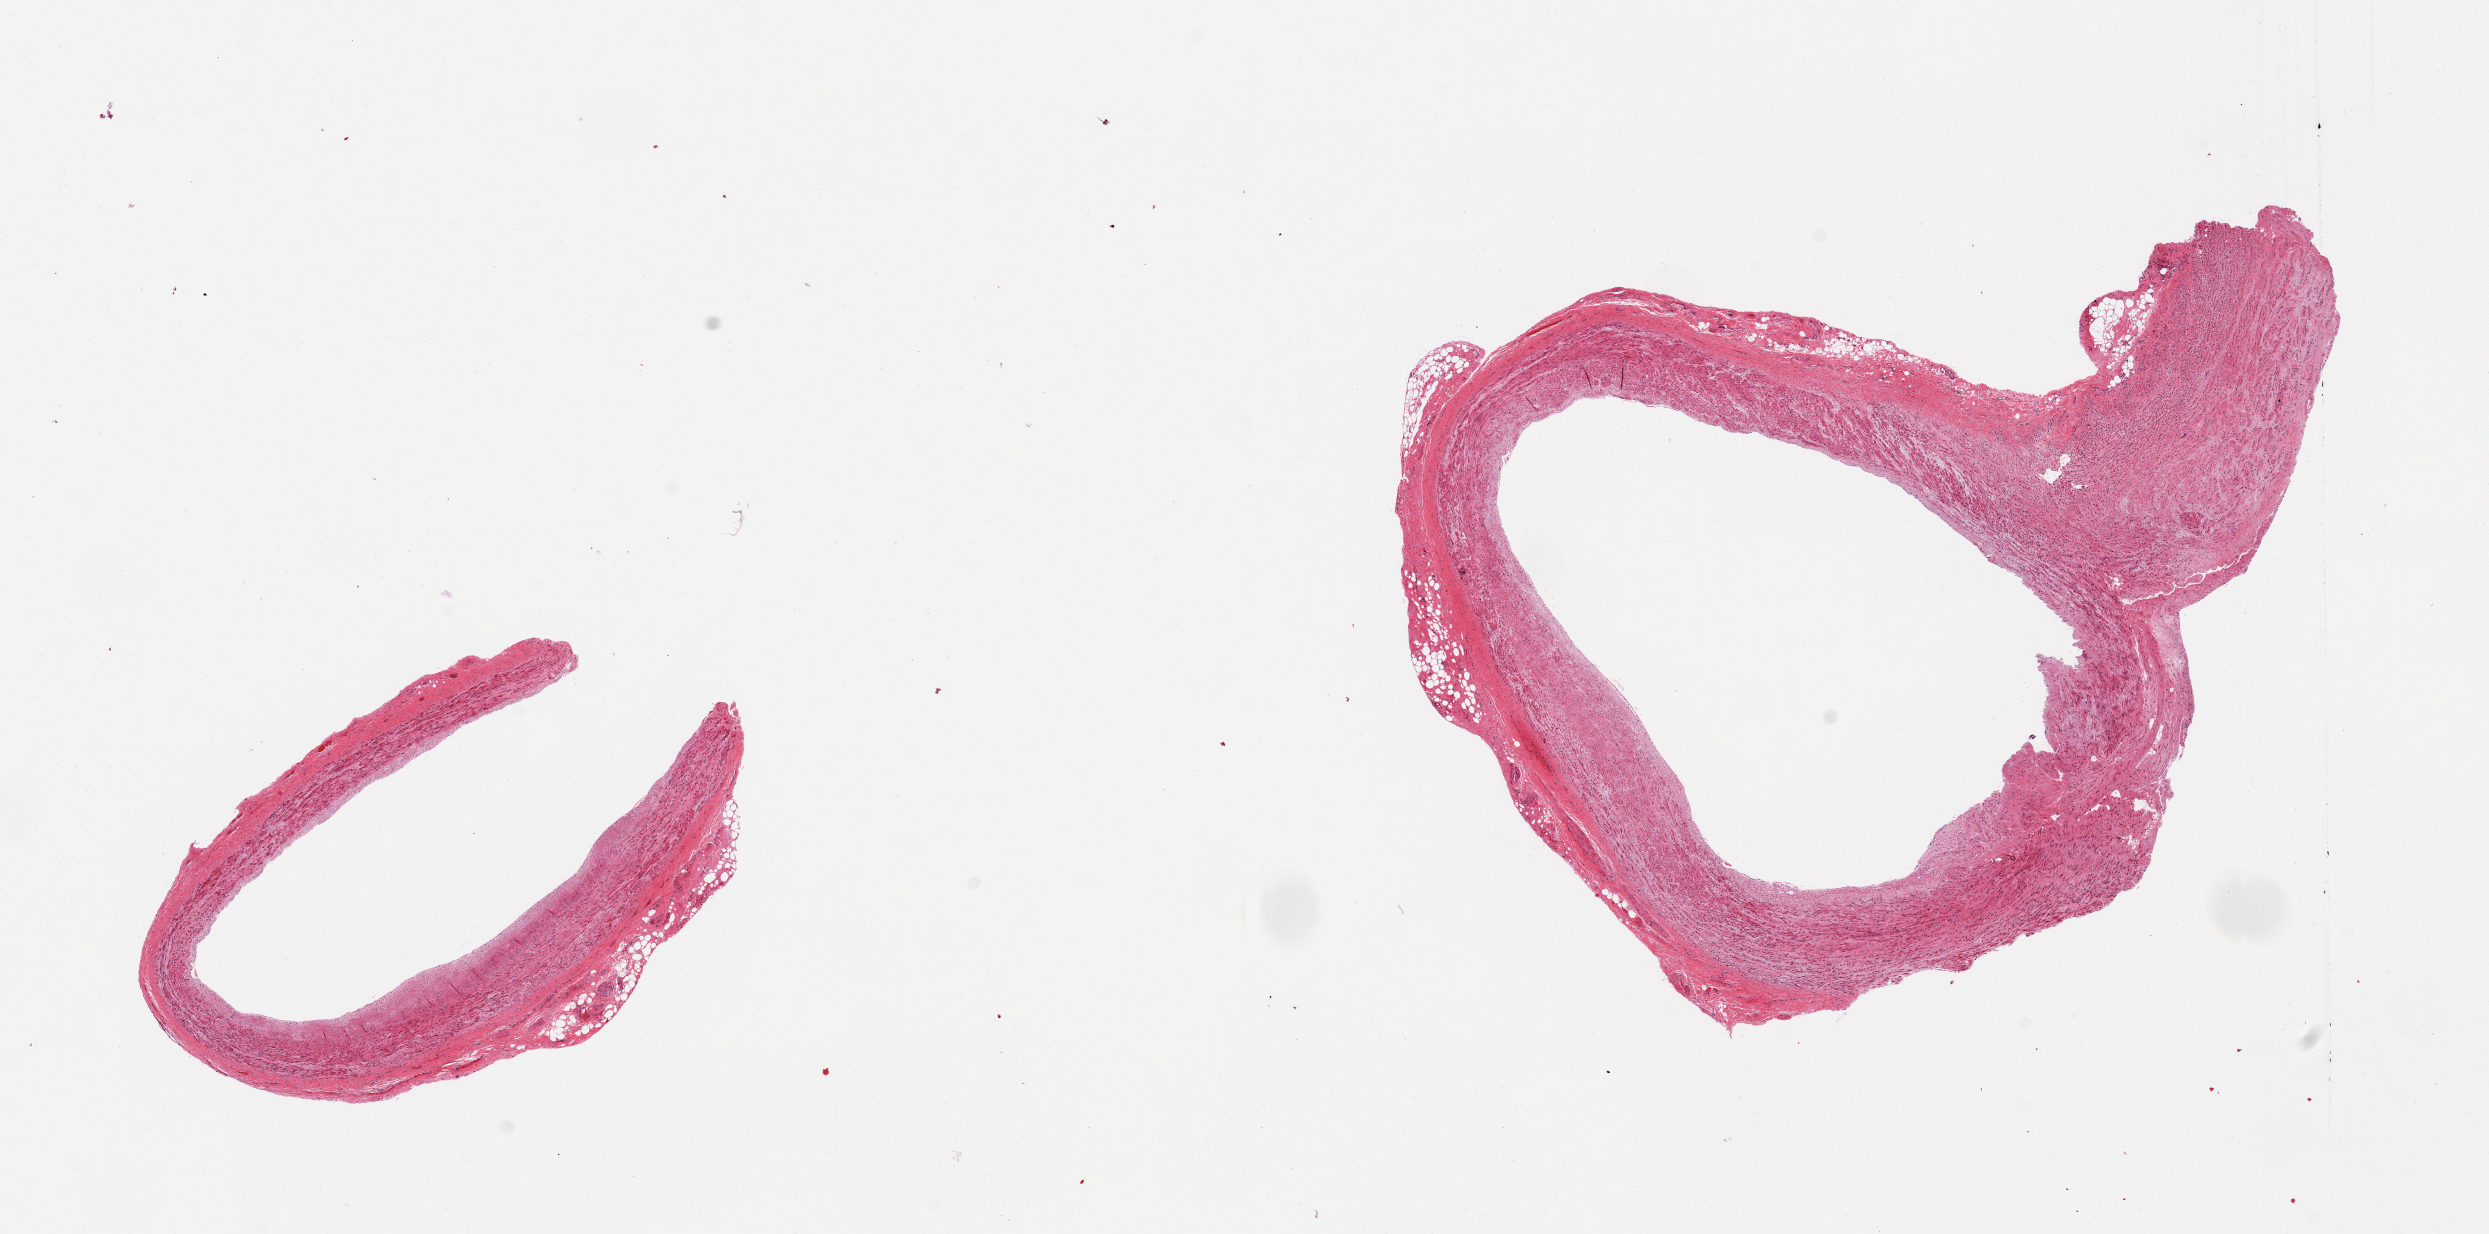
H&E whole-slide image, whole scanned area (about 19.7 x 9.8 mm, slide scanned at 20x) shown as a low-resolution overview. PAXgene-fixed paraffin-embedded (PFPE) section. Sampled site (target tissue): coronary artery. Tissue donor sample. Donor sex: female.
Reviewer comment on this tissue sample: 2 pieces; well trimmed.